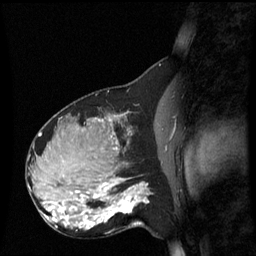
Breast MRI (dynamic contrast-enhanced), one sagittal slice. Dynamic contrast-enhanced series, image 2 of 3 at this slice position (ordered by acquisition). 1.5 T. TE 4.2 ms, TR 8.9 ms. 256 × 256 image matrix, field of view 220 × 220 mm. Patient: female, 31 years. From the clinical record (not read from this slice): setting: breast cancer imaged before/during neoadjuvant chemotherapy; receptor status: HR-positive, HER2-negative.
Annotated regions visible in this slice (semi-automatically segmented with operator editing):
- analysis volume of interest (the breast-tissue region the enhancement analysis was run in; not a lesion): box from (x=90, y=180) to (x=151, y=229) px
- tumour enhancement mask (voxels above the 70 % enhancement threshold inside the analysis volume of interest): (x=90, y=182)–(x=148, y=229)